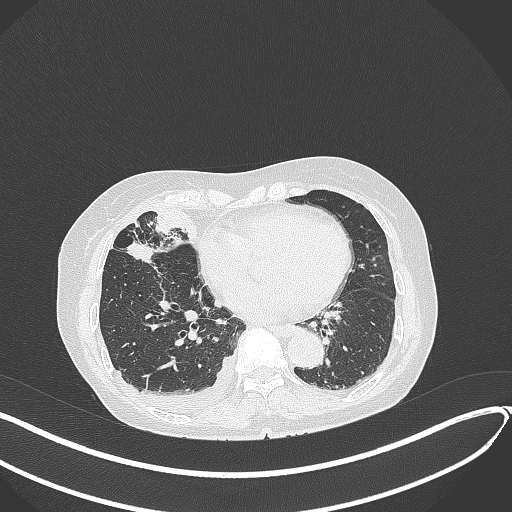
Chest CT, one axial slice; slice 148 of 418 in the series (ordered by position); reconstruction kernel B70f; 120 kVp; lung window (W 1500 / L -600 HU); 1 mm slice thickness; 512 × 512 image matrix, field of view 400 × 400 mm. Female patient, age 75 years. From the clinical record (not read from this slice): clinical TNM (as recorded): T2a N3 M0.
Structures marked on this image (rectangle marked by the reading radiologist):
- lung tumour (recorded histology: adenocarcinoma): bounding box <127,239,158,266> (left, top, right, bottom; pixels)